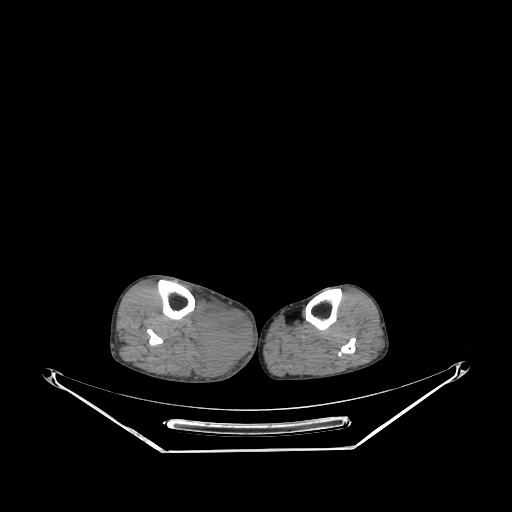
CT of an extremity soft-tissue mass (from a PET/CT study), one axial slice. Slice 132 of 267 in the series (ordered by position). Reconstruction kernel SOFT. 140 kVp. Soft-tissue window (W 400 / L 40 HU). 3.75 mm slice thickness. 512 × 512 image matrix, field of view 500 × 500 mm. Male patient. Case-level facts recorded for this patient, not image findings: histological type: pleiomorphic liposarcoma; grade: high; site of the primary tumour: right calf.
Structures marked on this image (expert contour drawn on MRI and transferred to this co-registered scan by the dataset authors):
- gross tumour volume including surrounding oedema: bounding box (x1, y1, x2, y2) in pixels: (198, 301, 254, 378)
- gross tumour volume (mass): (199, 306, 254, 362)